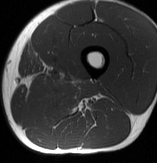
MRI of an extremity soft-tissue mass, one axial slice; slice 22 of 70 in the series (ordered by position); MR volume resampled by the dataset authors to the PET/CT grid (not the native acquisition matrix); 3.27 mm slice thickness; 157 × 163 image matrix, field of view 153 × 159 mm. Male patient. Case-level facts recorded for this patient, not image findings: histological type: extraskeletal osteosarcoma; grade: high; site of the primary tumour: left adductur.
Structures marked on this image (expert contour drawn on MRI and transferred to this co-registered scan by the dataset authors):
- gross tumour volume (mass): bounding box [x1, y1, x2, y2] px = [26, 76, 100, 105]